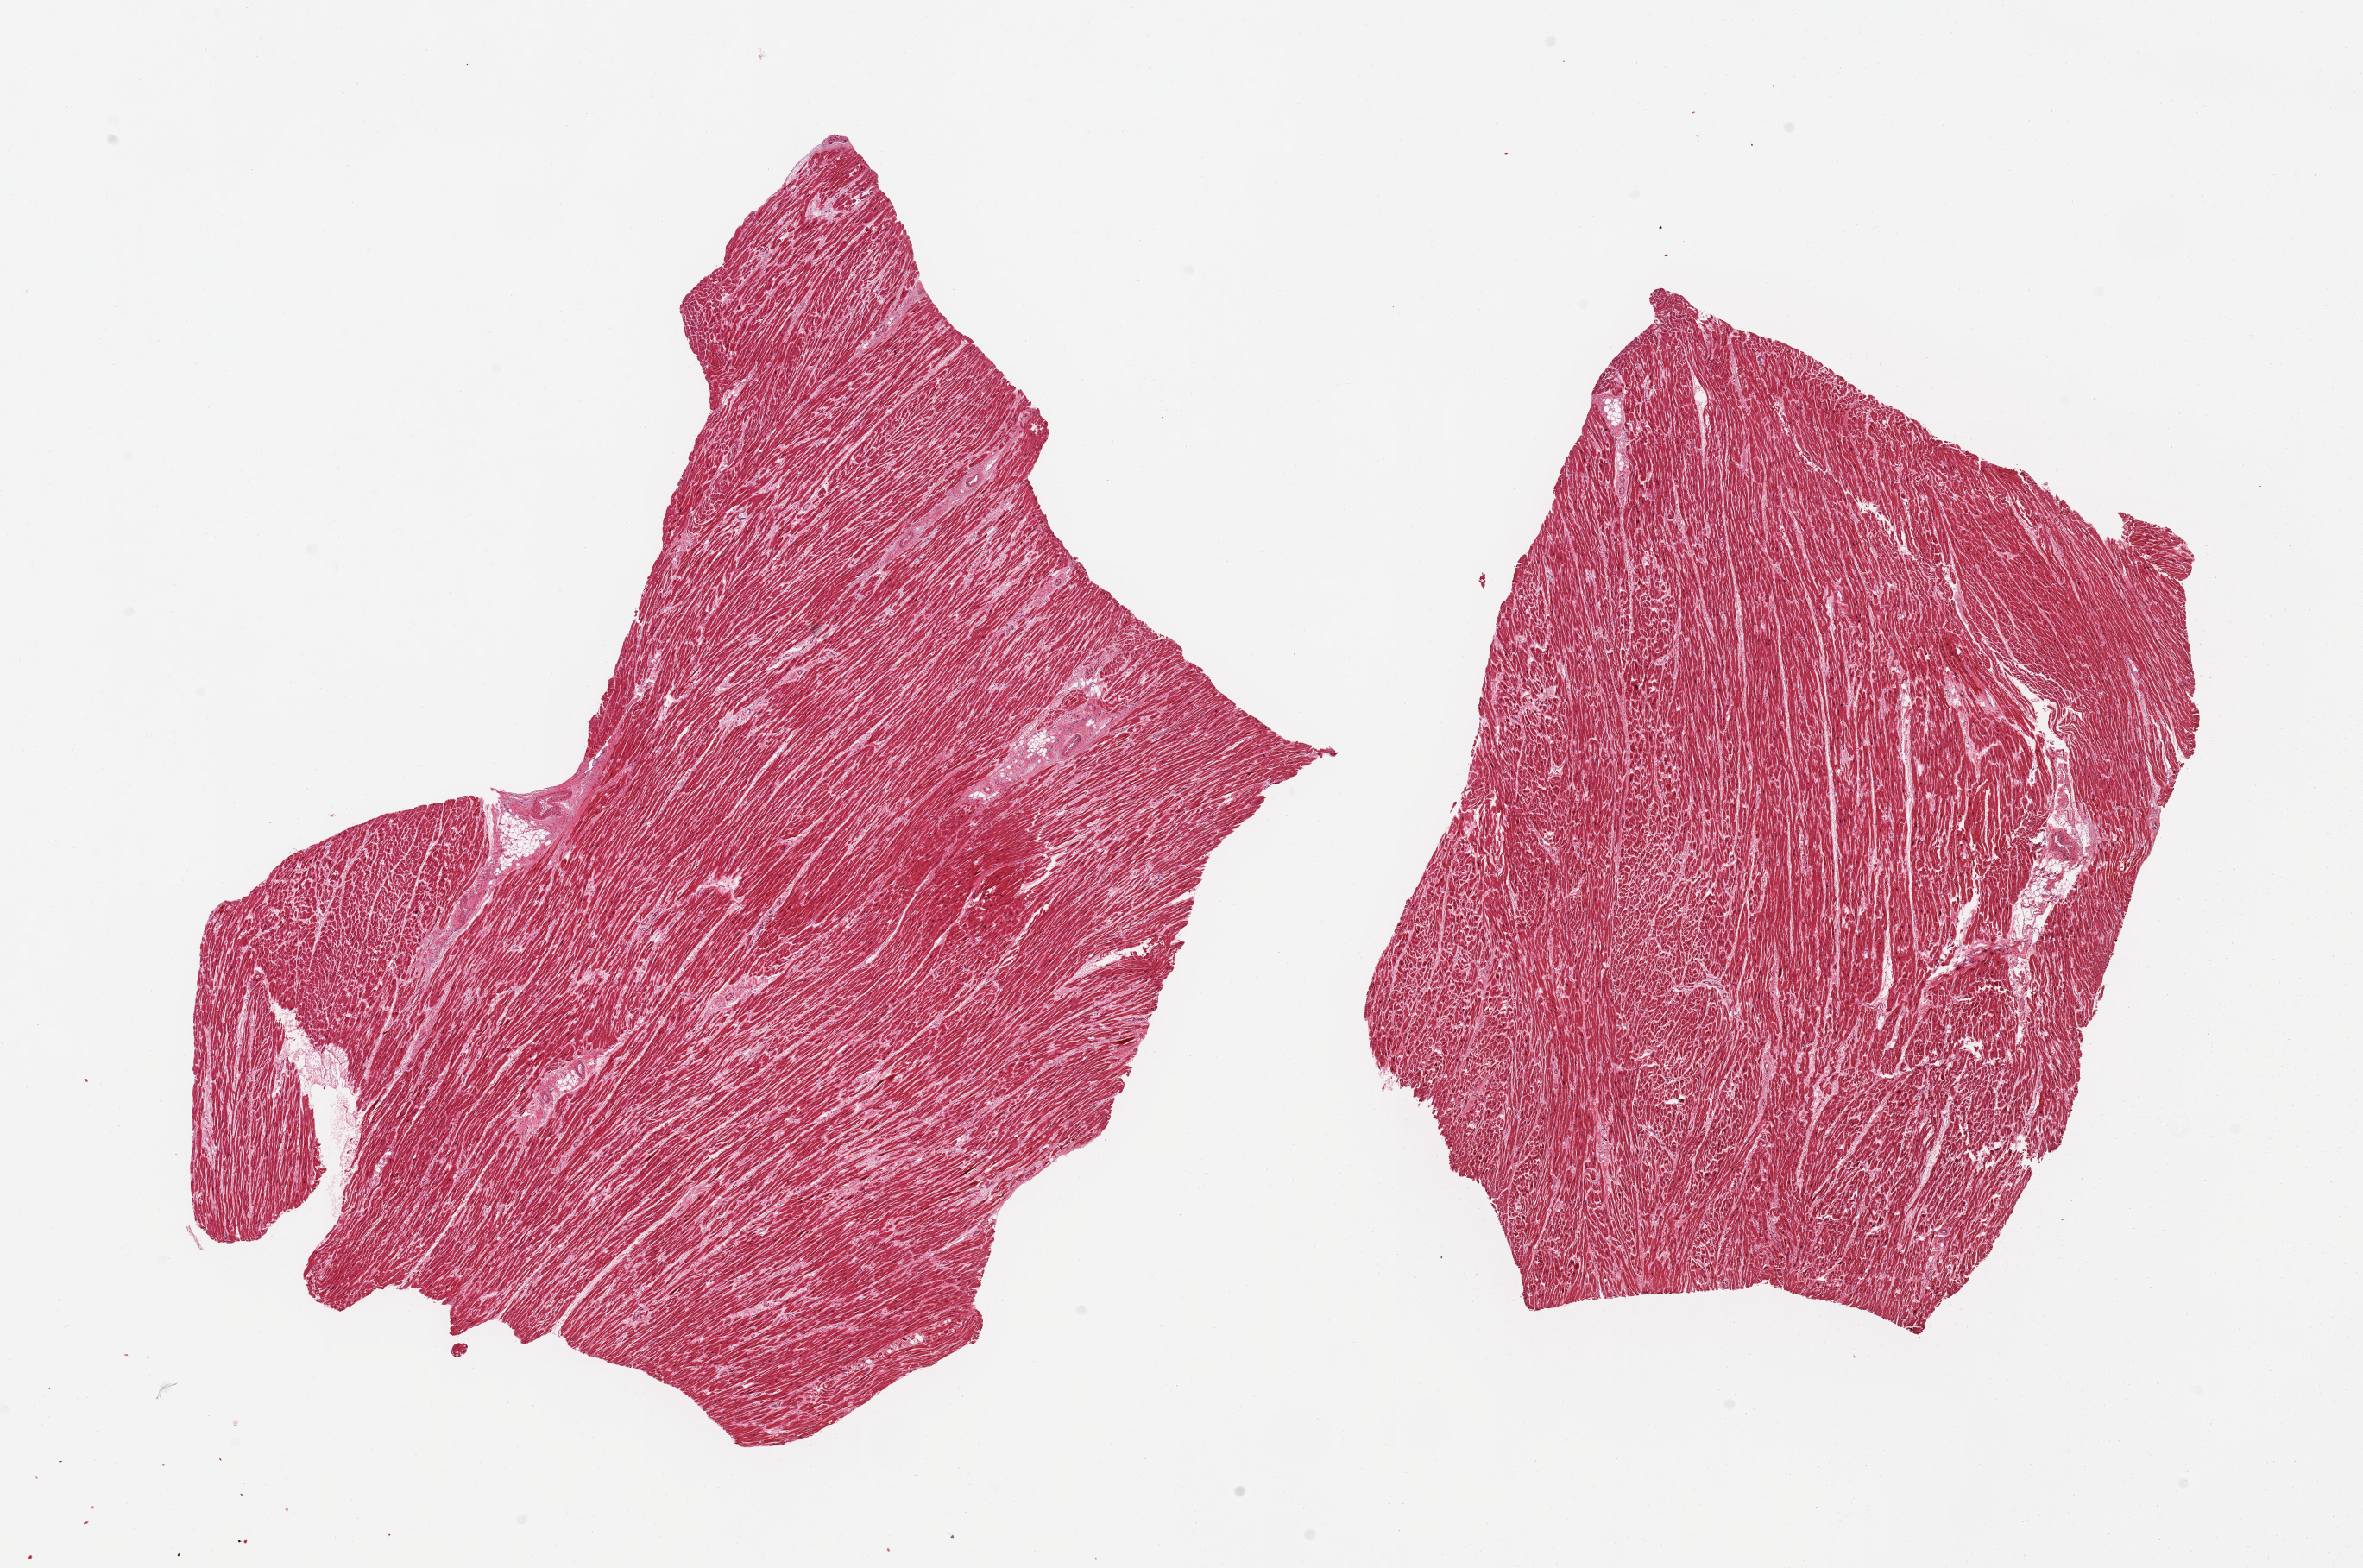
Hematoxylin and eosin (H&E) whole-slide image — whole scanned area (about 21.7 x 14.4 mm) shown as a low-resolution overview, PAXgene-fixed paraffin-embedded (PFPE) section, target tissue: heart, donor tissue sample. Female donor.
Pathologist's review note for this sample: 2 pieces, mild-moderate interstitial fibrosis/chronic ischemic changes.